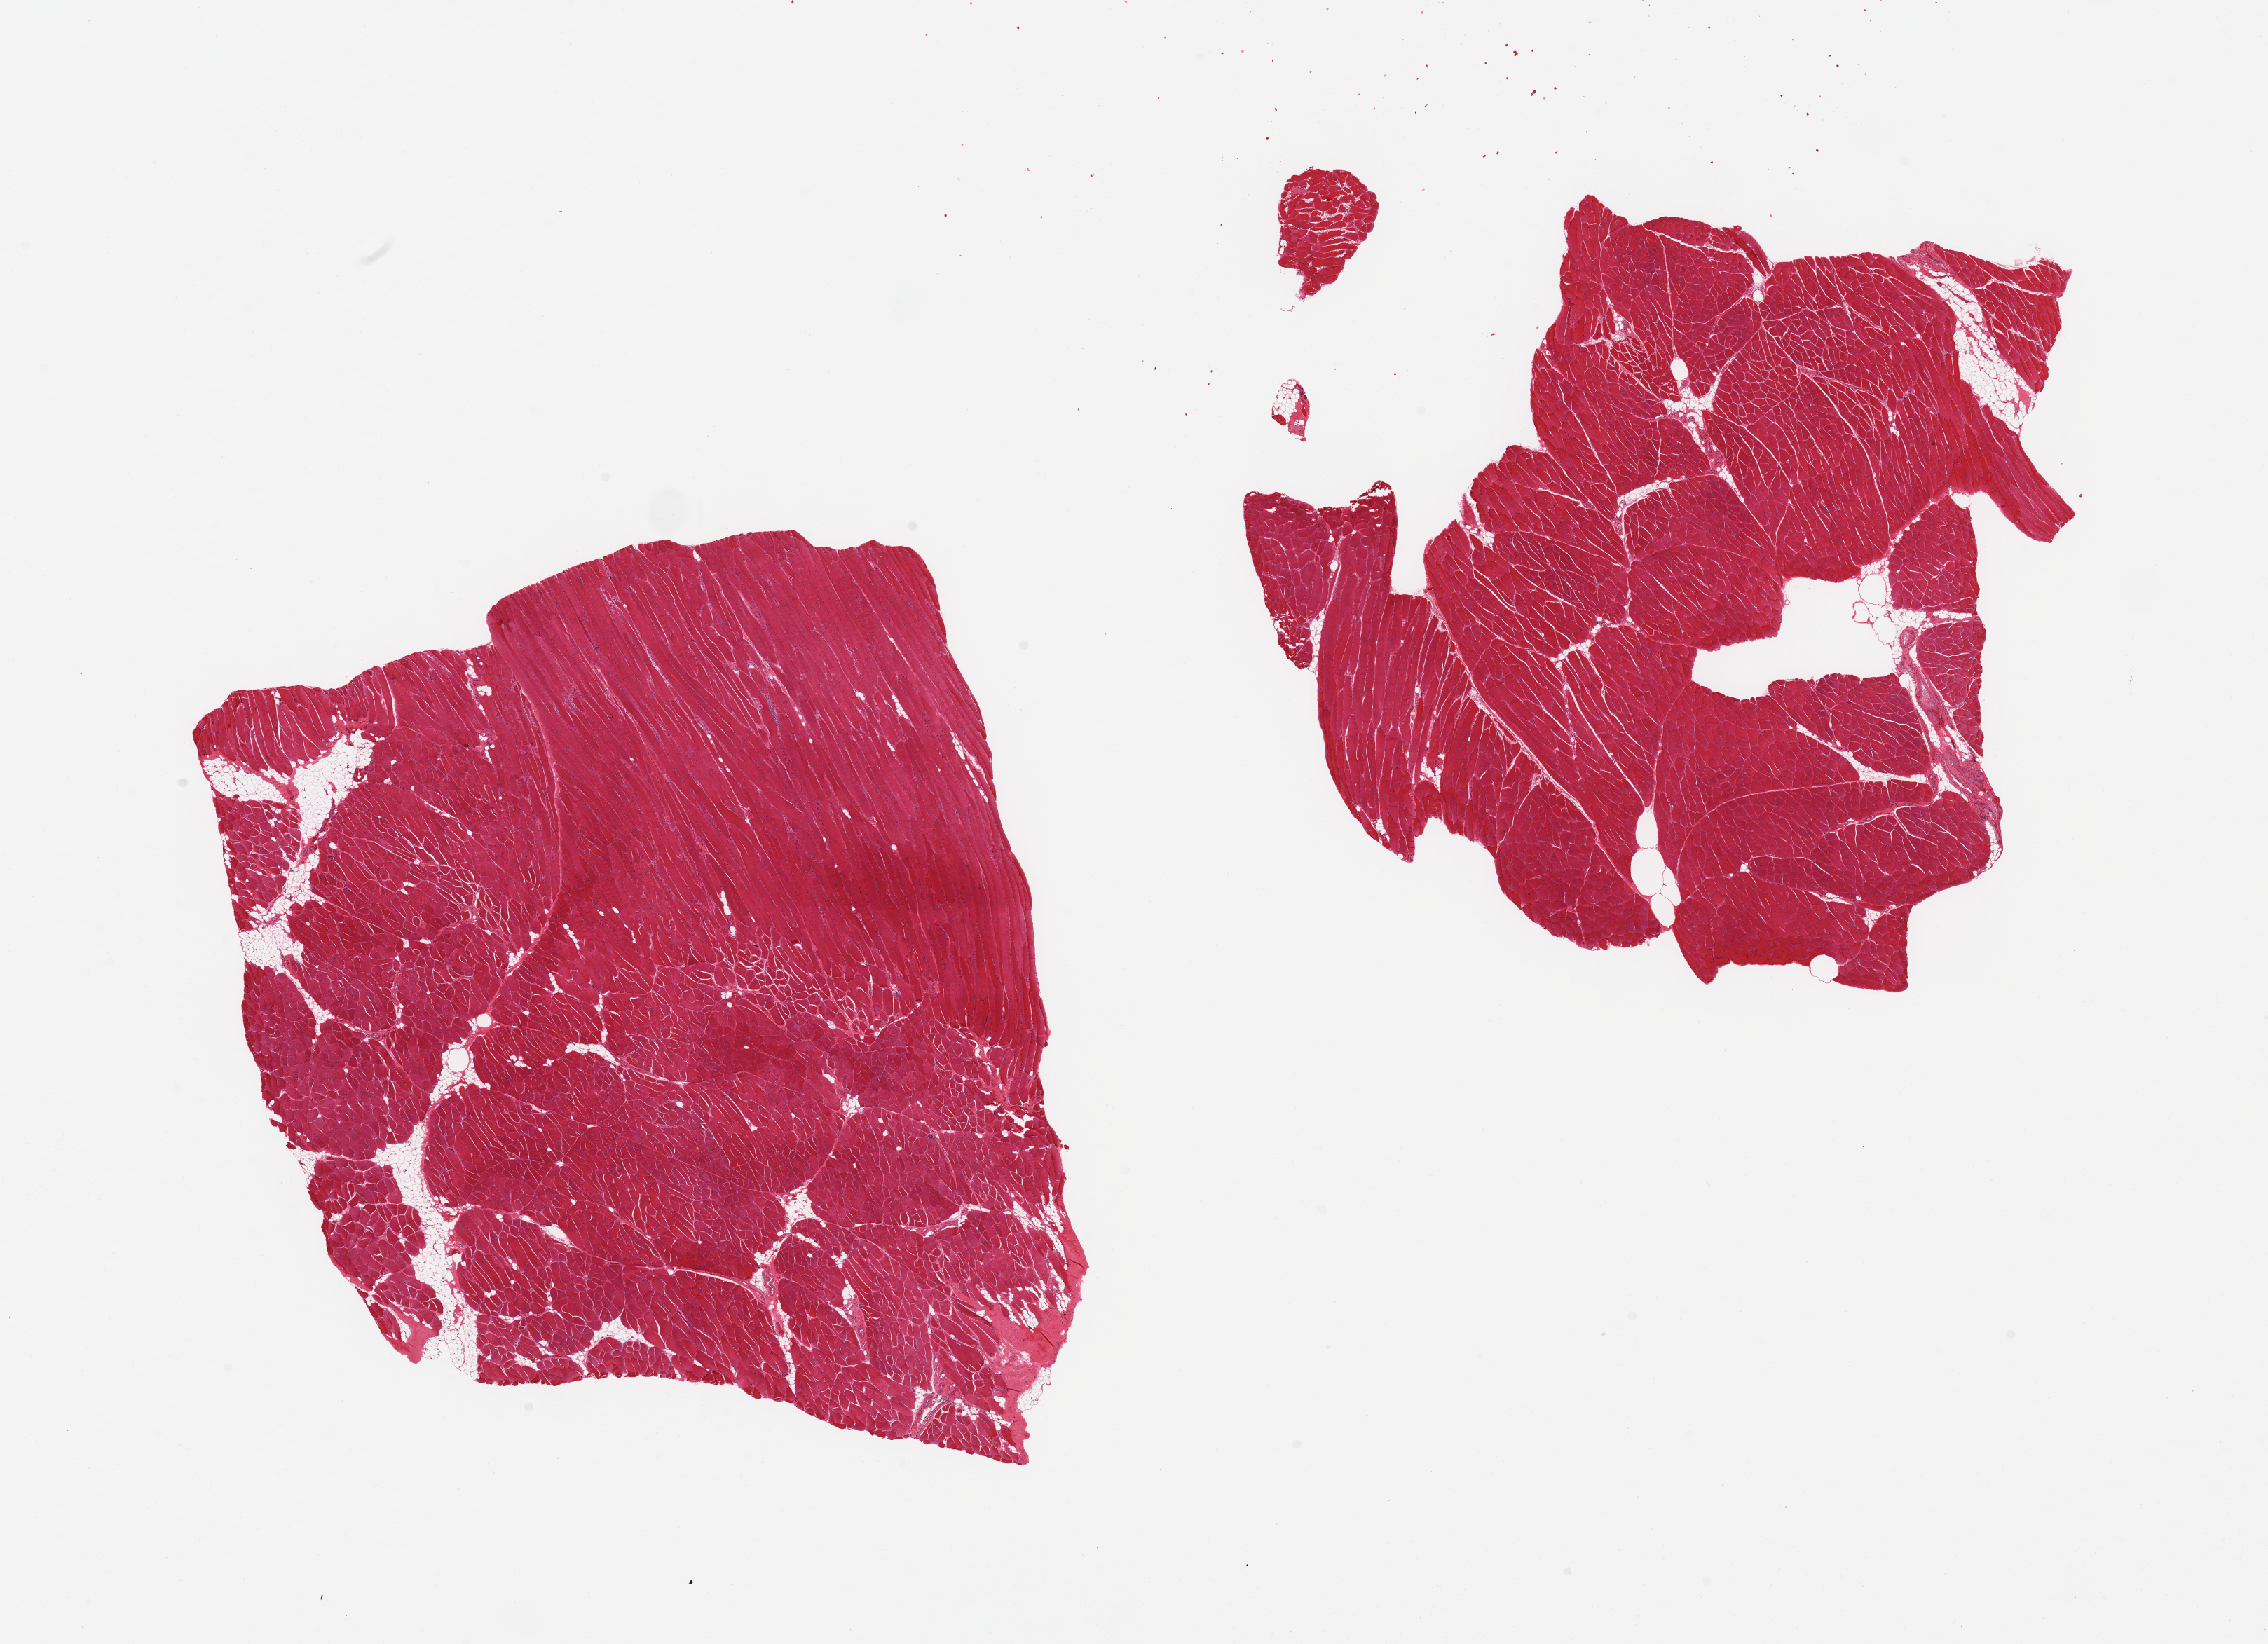
Hematoxylin and eosin (H&E) whole-slide image, low-resolution overview of the scanned area, about 25.6 x 18.6 mm (slide scanned at 20x), PAXgene-fixed, paraffin-embedded tissue, target tissue: skeletal muscle, tissue donor sample. Male donor.
Pathologist's review note for this sample: 2 pieces; no more than 10% internal fat, small portion of tendon.